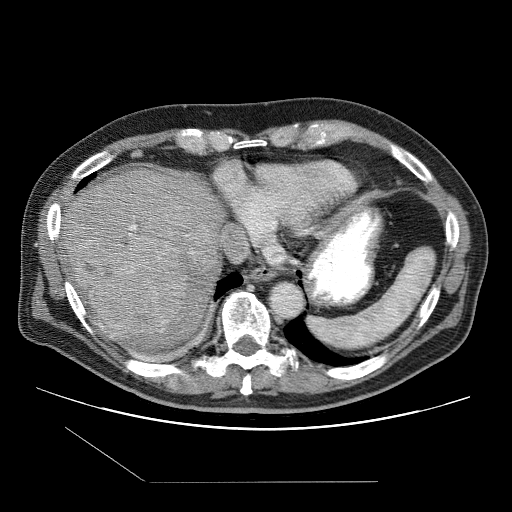
Contrast-enhanced abdominal CT (liver protocol), one axial slice; position 87 of 109 along the scan axis; reconstruction kernel STANDARD; one of 2 acquisitions stored at this slice position; soft-tissue window (W 400 / L 40 HU); 2.5 mm slice thickness; 512 × 512 image matrix, field of view 400 × 400 mm. Case-level facts recorded for this patient, not image findings: diagnosis: hepatocellular carcinoma (patient treated with transarterial chemoembolisation; whether this scan precedes or follows treatment is not stated here); TNM stage (as recorded): Stage-IIIB; Child-Pugh class: A; tumour nodularity: multinodular.
Annotated regions visible in this slice (semi-automatically segmented with operator editing):
- liver parenchyma outside the tumour (the mass and vessels are separate outlines, so this box may not span the whole liver): box from (x=60, y=168) to (x=272, y=346) px
- mass: (x=72, y=233)–(x=189, y=339)
- liver vessels: (x=129, y=225)–(x=260, y=254)